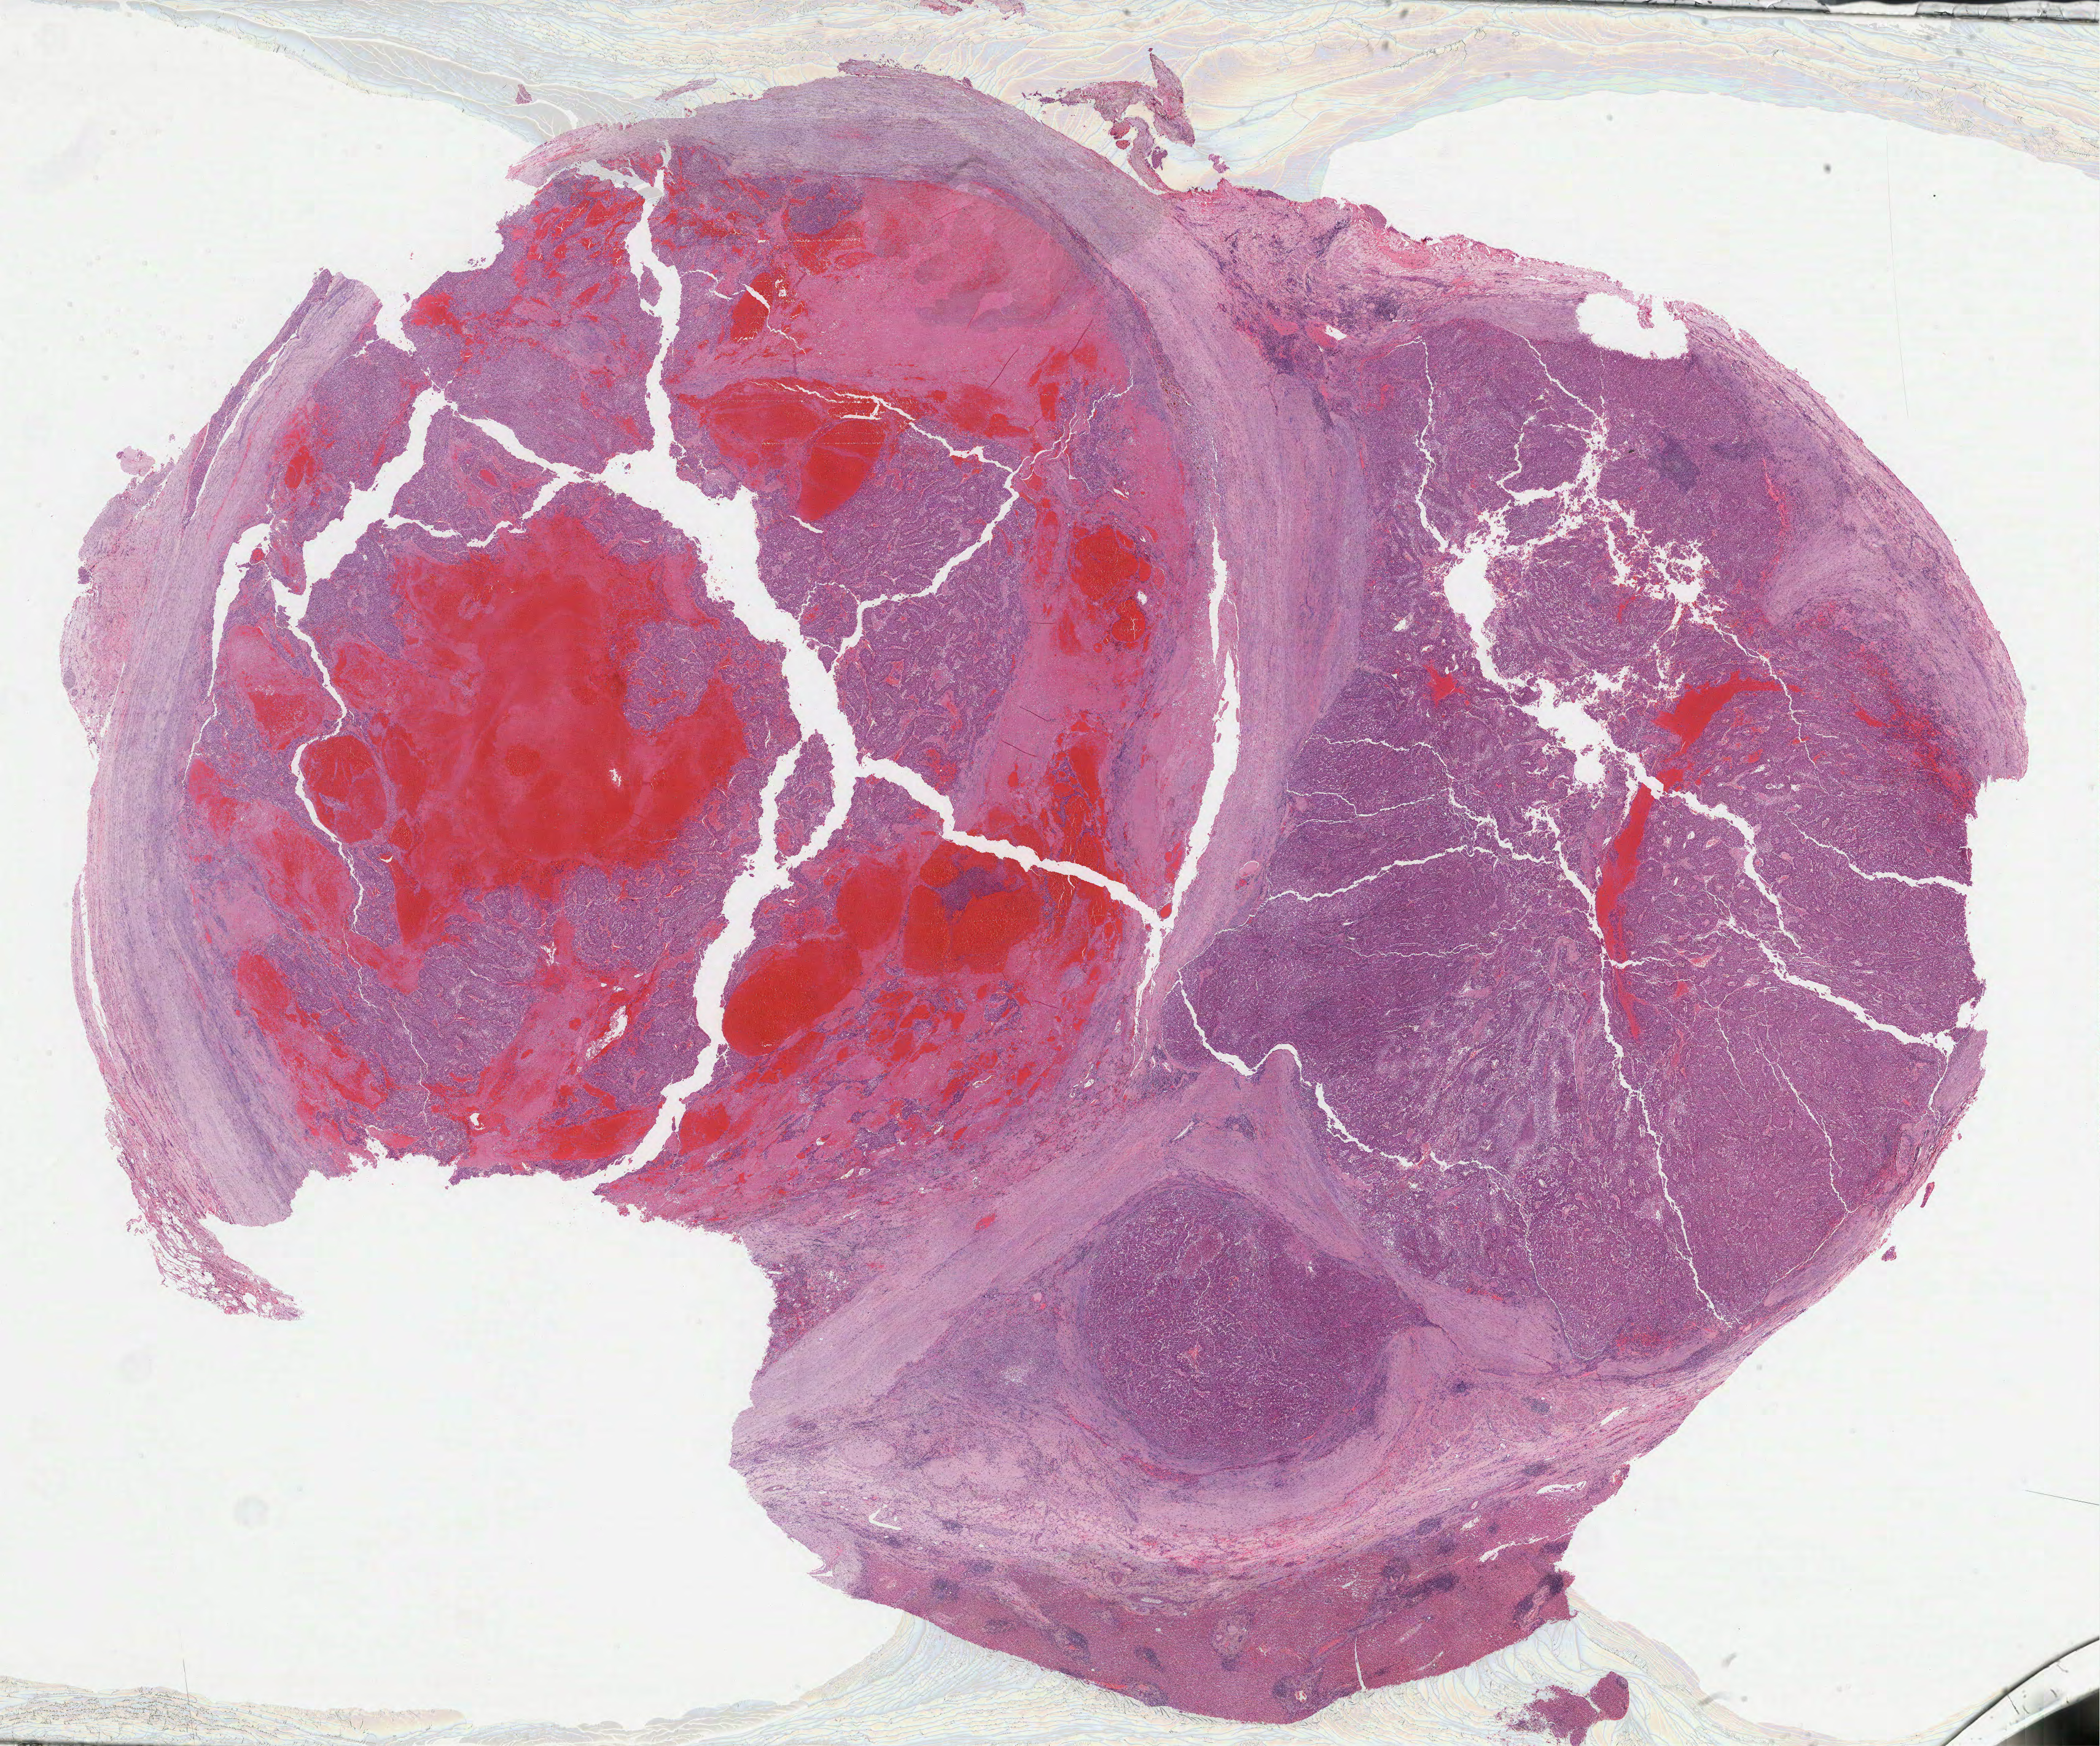
Whole-slide histology image, Hematoxylin and eosin (H&E) stained, low-resolution overview of the scanned area, about 27.6 x 23.0 mm (slide scanned at 40x), formalin-fixed paraffin-embedded (FFPE) diagnostic section, sample: primary tumour, liver. Patient: male, age at initial diagnosis 49 years. Histologic grade: G1 (well differentiated).
- AJCC pathologic stage: IIIA (6th edition)
- diagnosis: Hepatocellular carcinoma, NOS